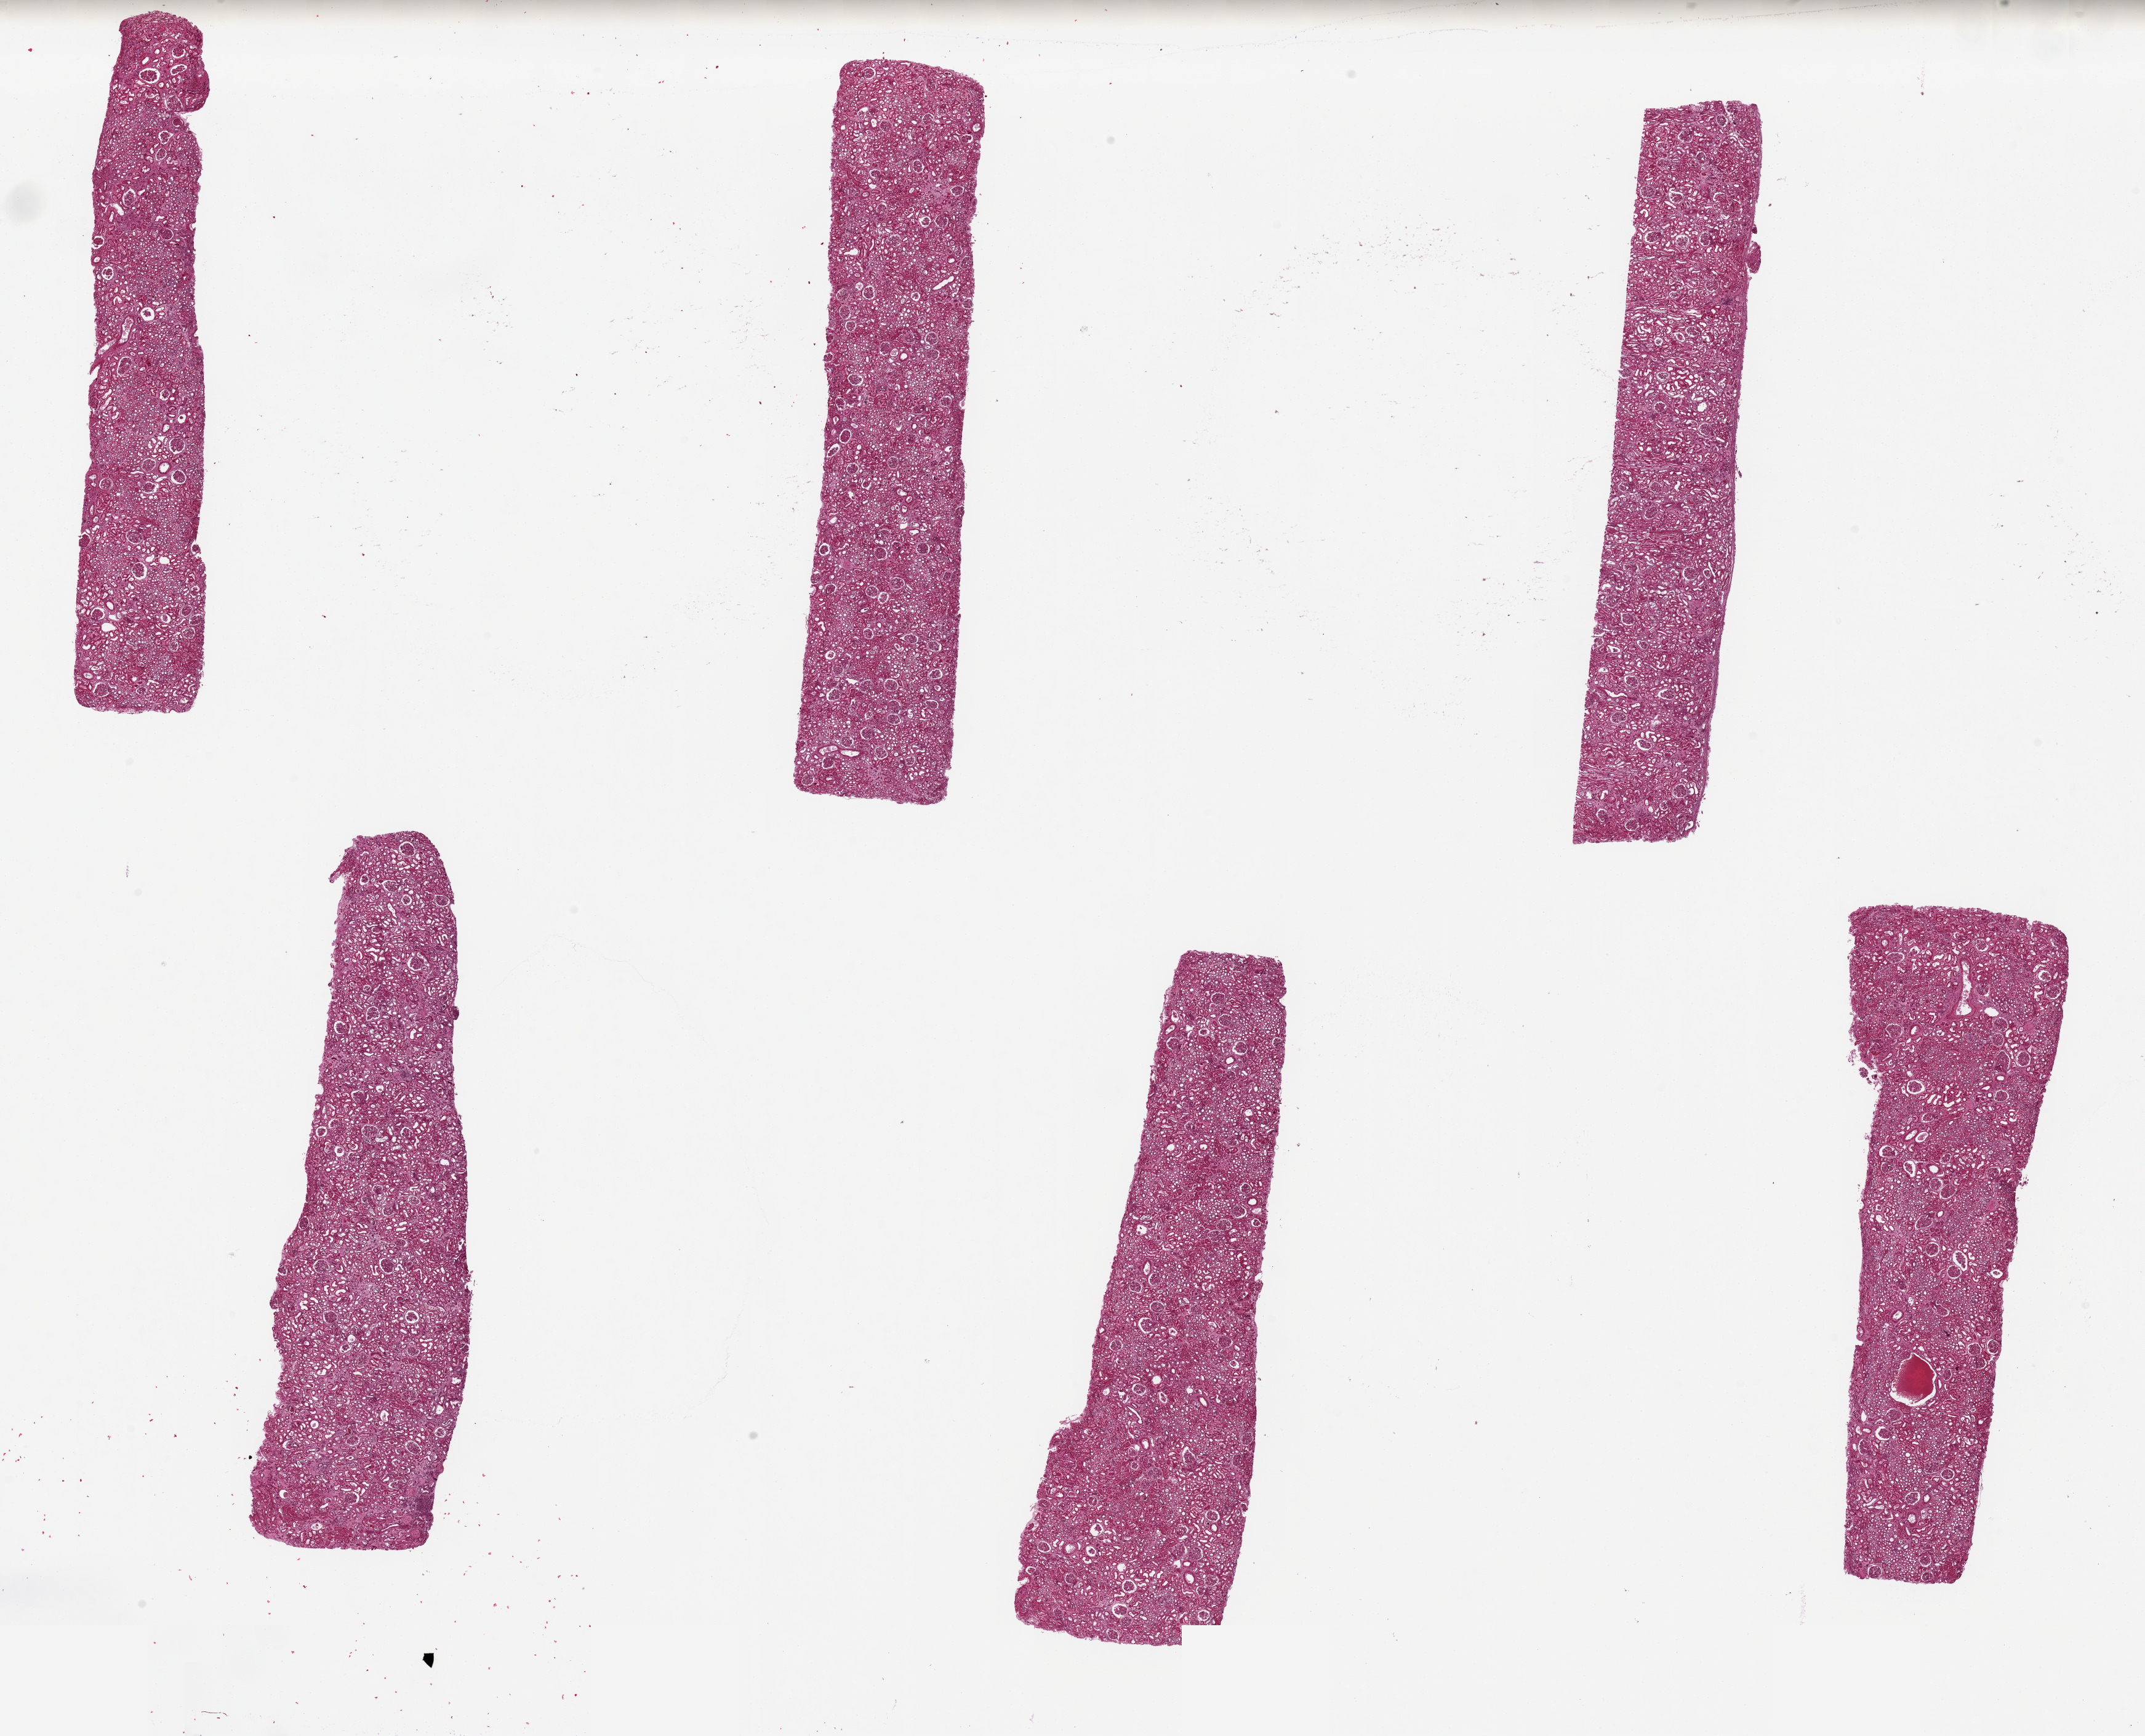
Whole-slide image, hematoxylin and eosin (H&E) stain, low-resolution overview of the scanned area, about 27.6 x 22.3 mm, PAXgene-fixed, paraffin-embedded tissue, section of renal cortex (target tissue), tissue donor sample. Donor: male.
Pathologist's review note for this sample: 6 pieces, up to 9.5x2mm; all cortex.